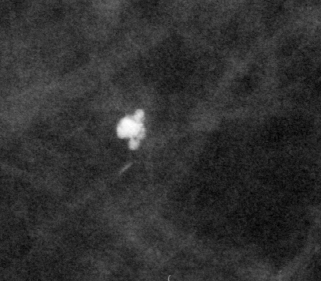
Cropped region of a digitized screen-film mammogram centred on a radiologist-marked abnormality, left breast, CC view.
Finding: calcifications, morphology coarse; BI-RADS assessment category 2; subtlety rating 5 on a 1 (subtle) to 5 (obvious) scale; benign without callback (not worked up further).